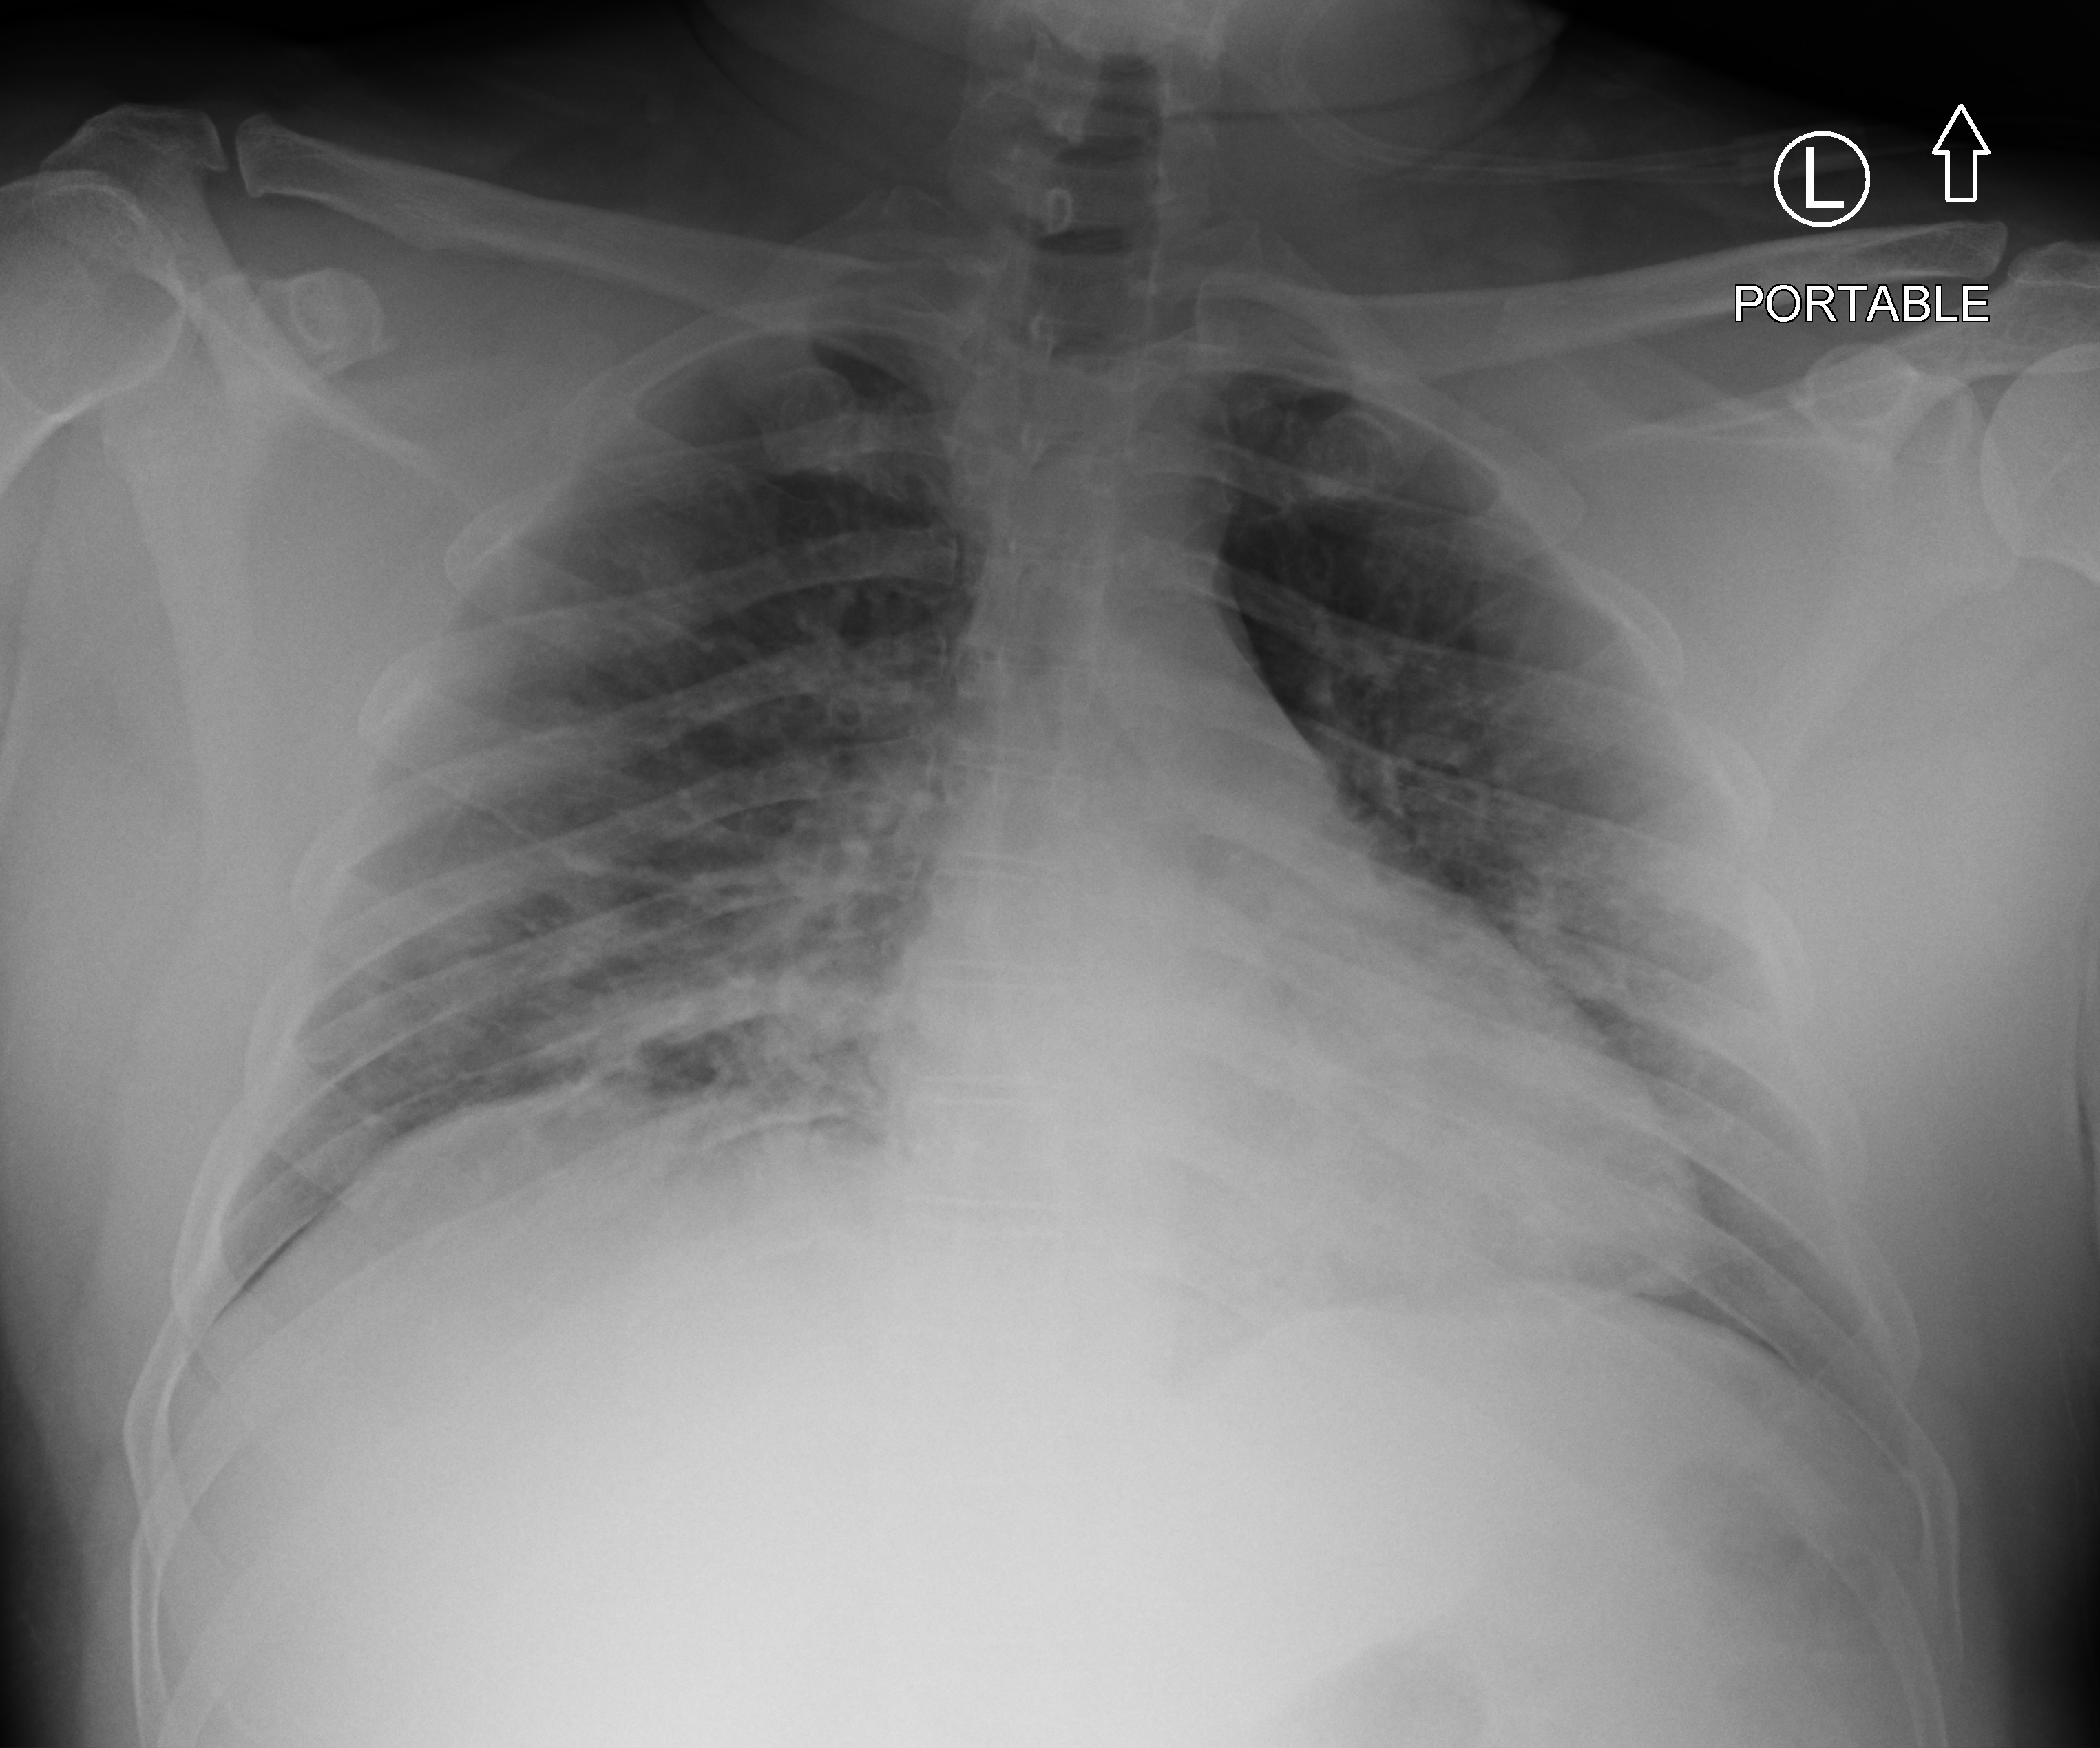
Bedside chest radiograph (computed radiography), anteroposterior (AP) projection. Patient hospitalised with COVID-19, aged 18–59 years.
From the hospital-stay record, not from the radiograph (when in the stay this image was taken is not recorded): admitted to intensive care during this hospital stay: yes; mechanically ventilated during this hospital stay: yes.